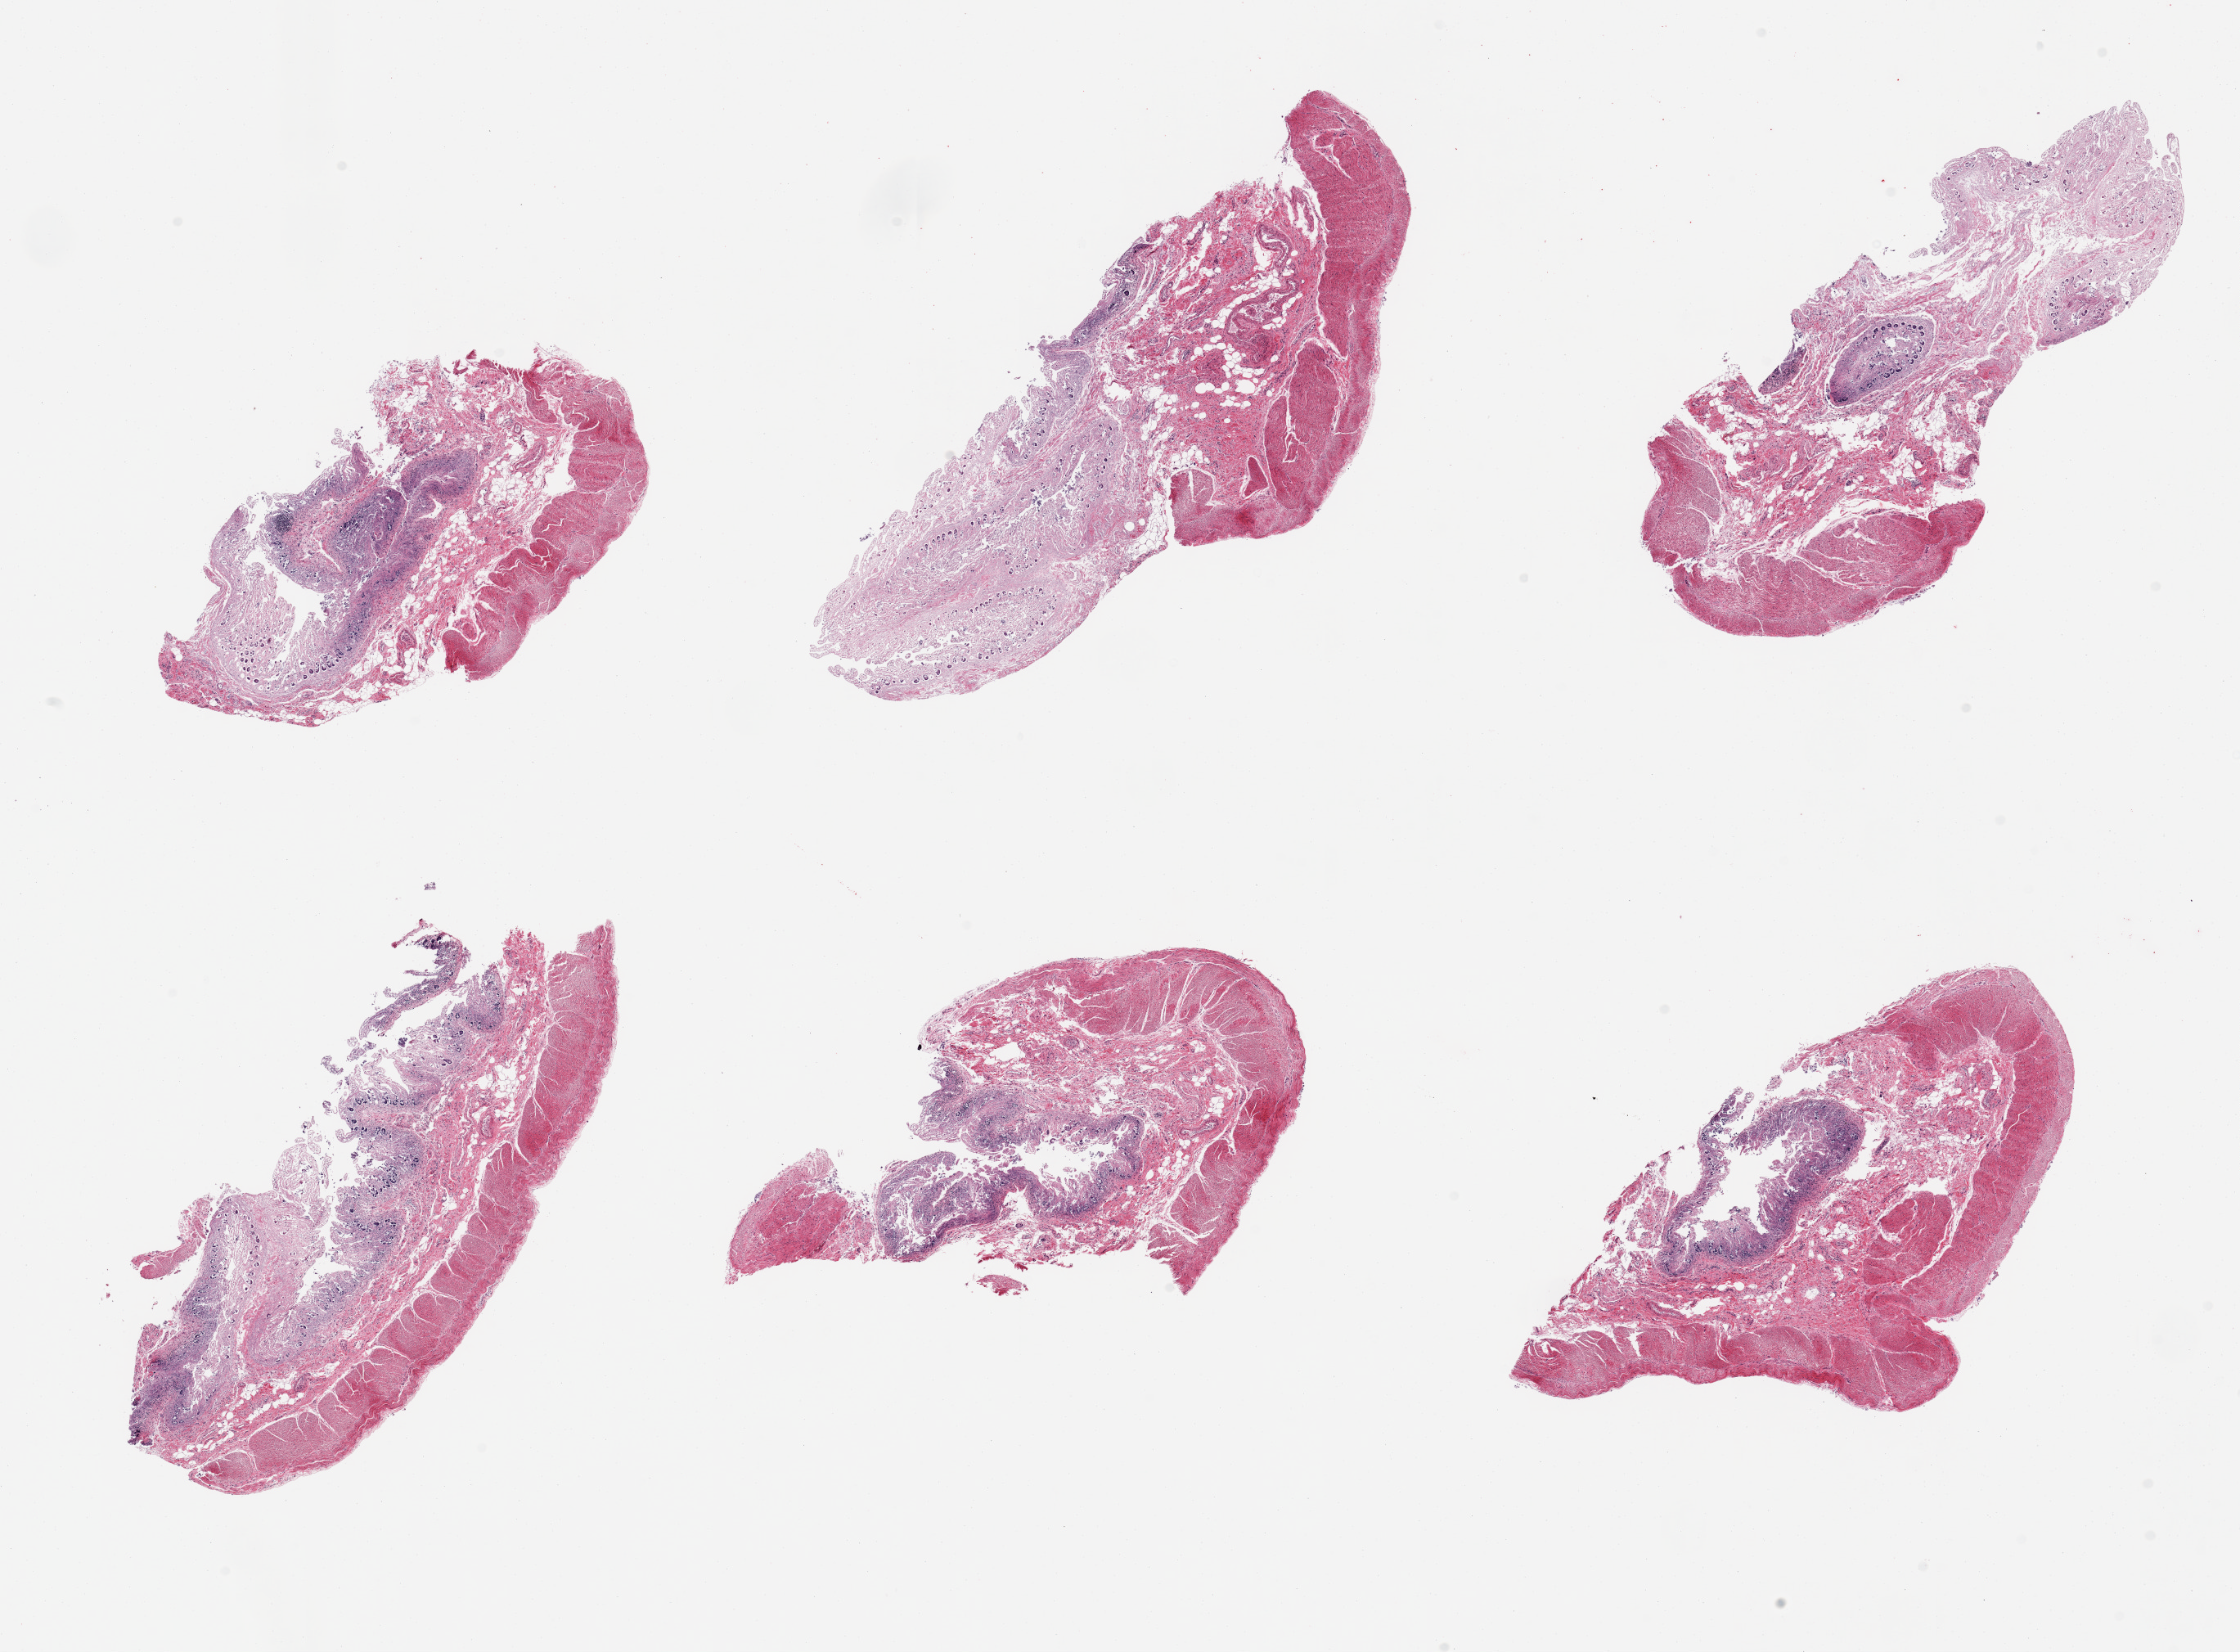
Haematoxylin and eosin whole-slide image, whole scanned area (about 21.7 x 16.0 mm) shown as a low-resolution overview, PAXgene-fixed, paraffin-embedded tissue, section of ileum (target tissue), tissue donor sample. Male donor.
• pathologist's review note for this sample: 6 pieces; autolyzed mucosa with no significant residual lymphoid component, muscularis present (not target)